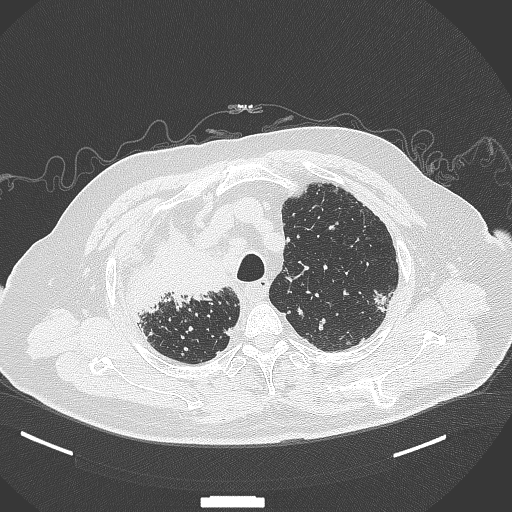
Chest CT, one axial slice. Slice 293 of 384 in the series (ordered by position). Reconstruction kernel B70f. 120 kVp. Lung window (W 1500 / L -600 HU). 512 × 512 image matrix, field of view 400 × 400 mm. Patient: male, 69 years. Case-level facts recorded for this patient, not image findings: clinical TNM (as recorded): T4 N3 M1.
Structures marked on this image (bounding box drawn by a radiologist):
- lung tumour (recorded histology: adenocarcinoma): bounding box [x1, y1, x2, y2] px = [125, 218, 237, 319]